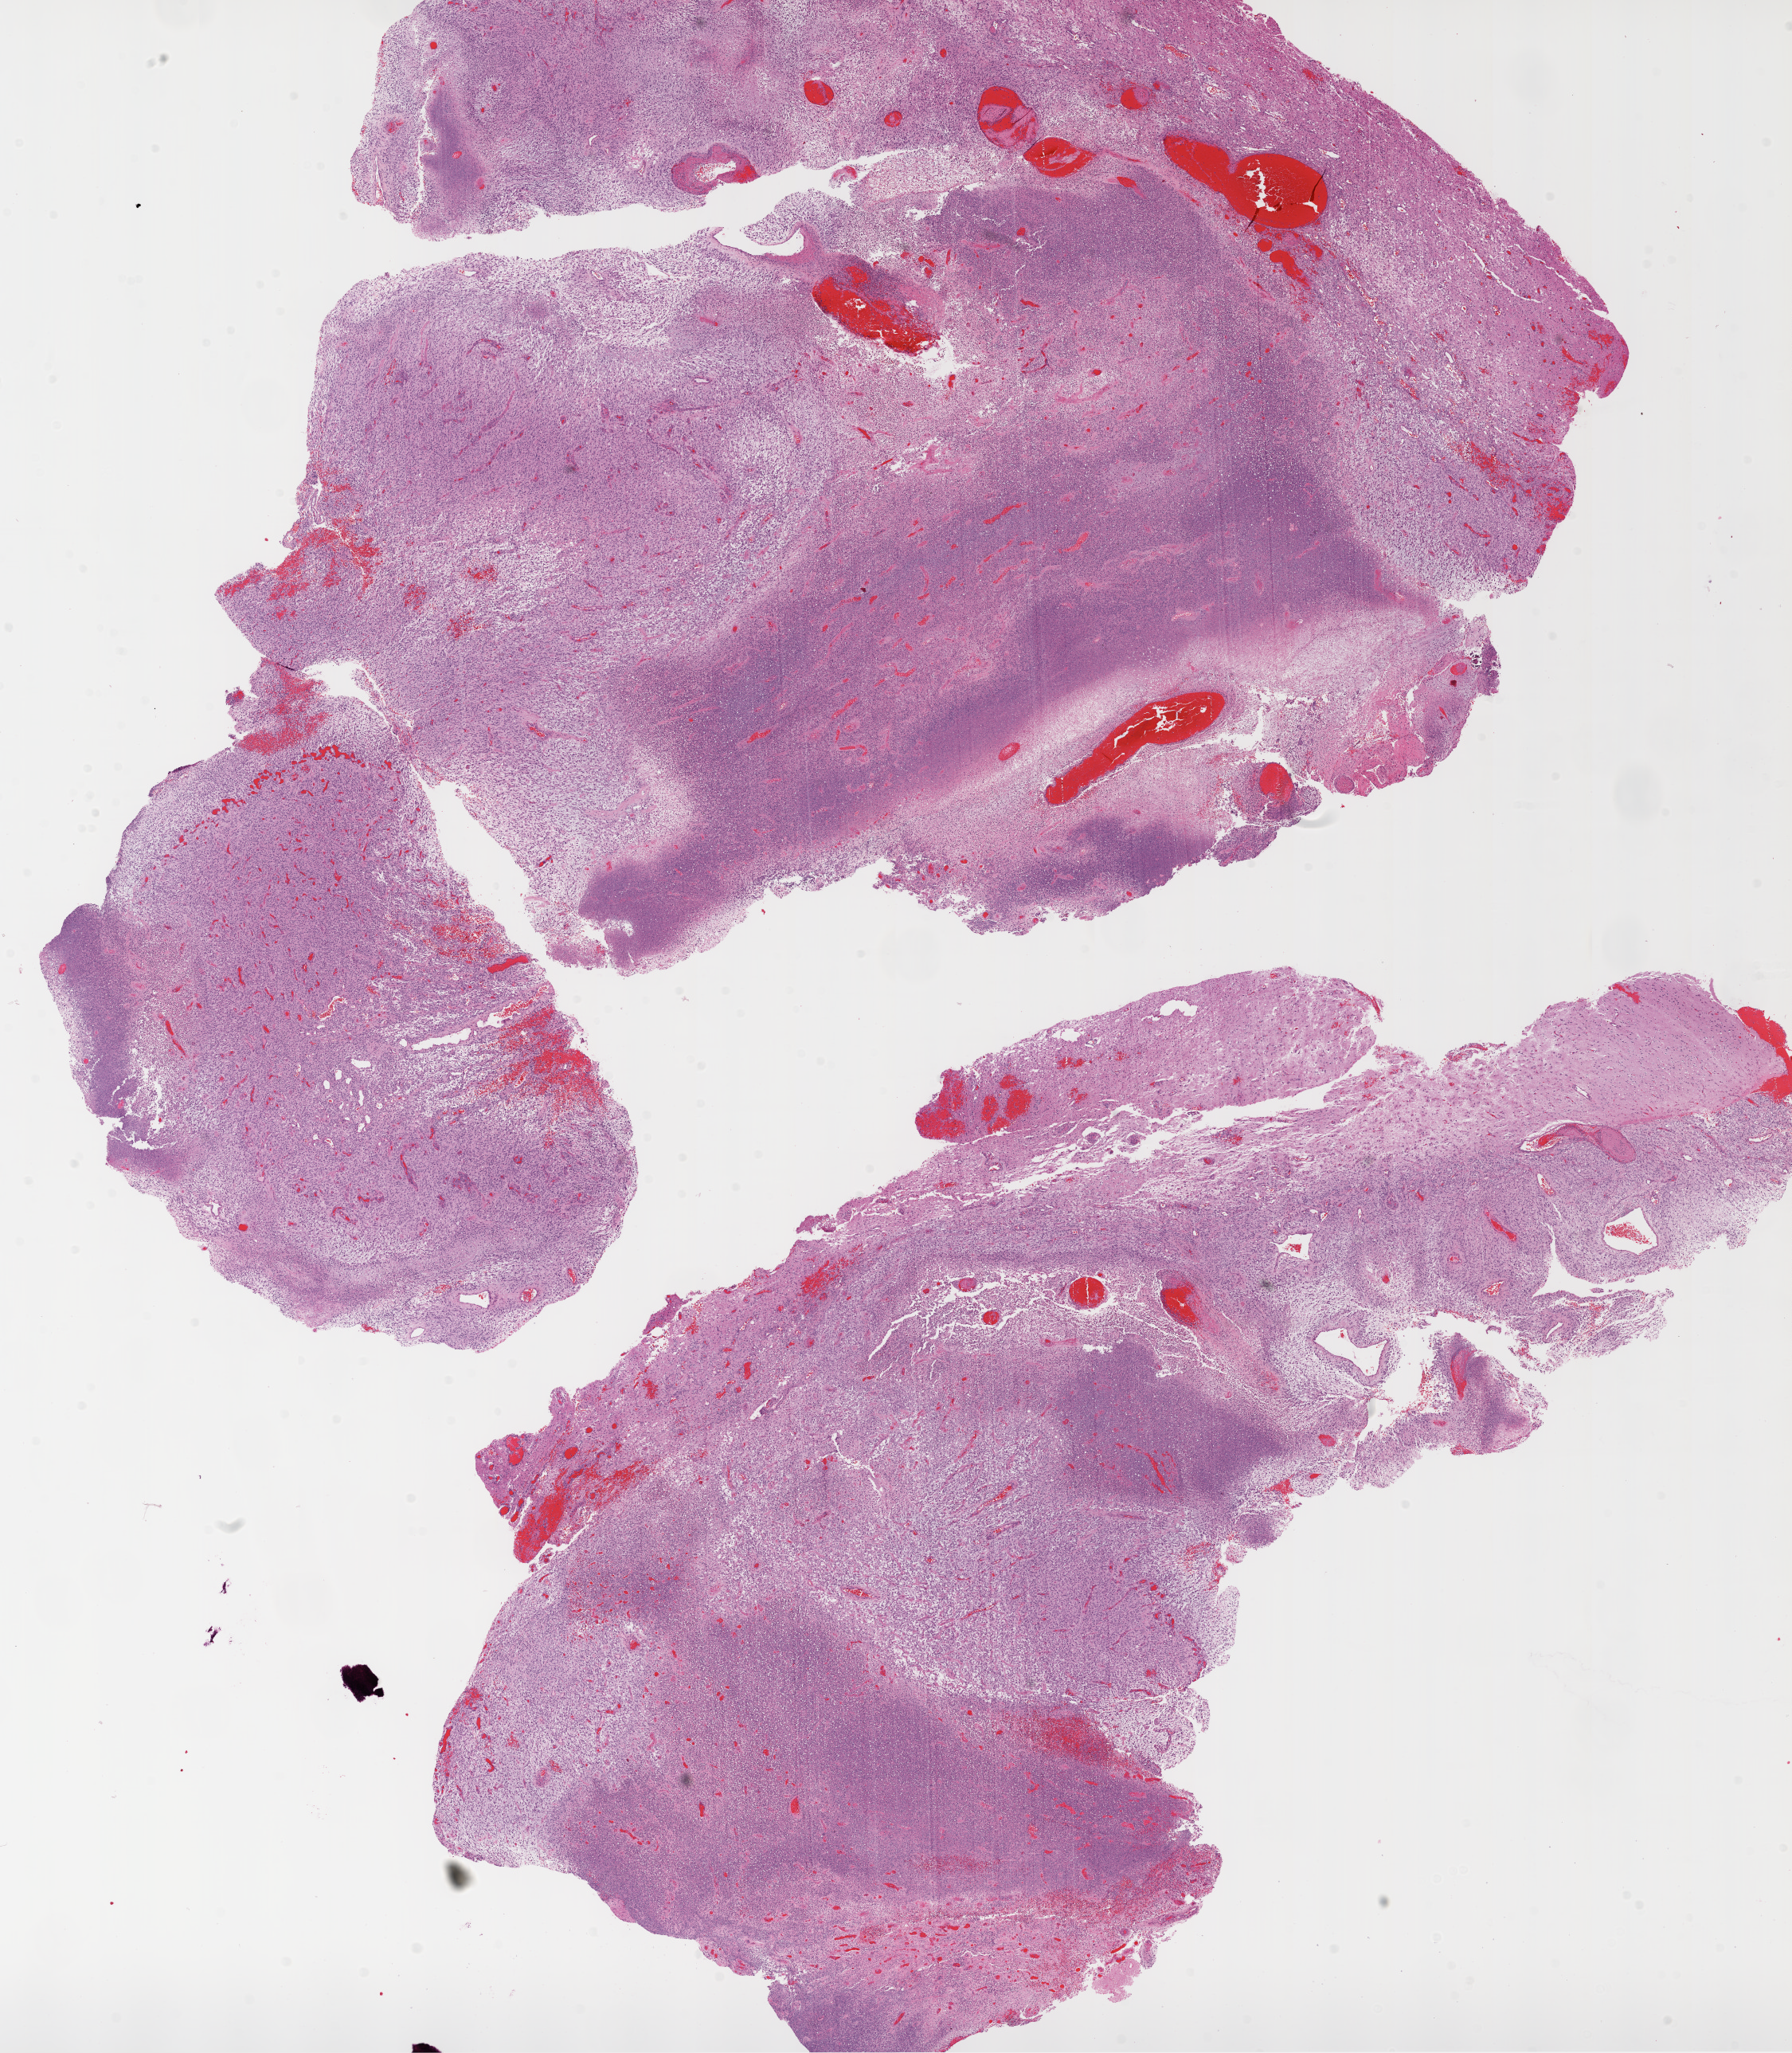
Digitized Hematoxylin and eosin (H&E) stained tissue section (whole slide) — shown as a low-resolution overview of the whole scanned area (about 18.1 x 20.7 mm). FFPE section. Brain, primary tumour sample. Female patient; age at initial diagnosis 61 years.
* histologic diagnosis: Glioblastoma